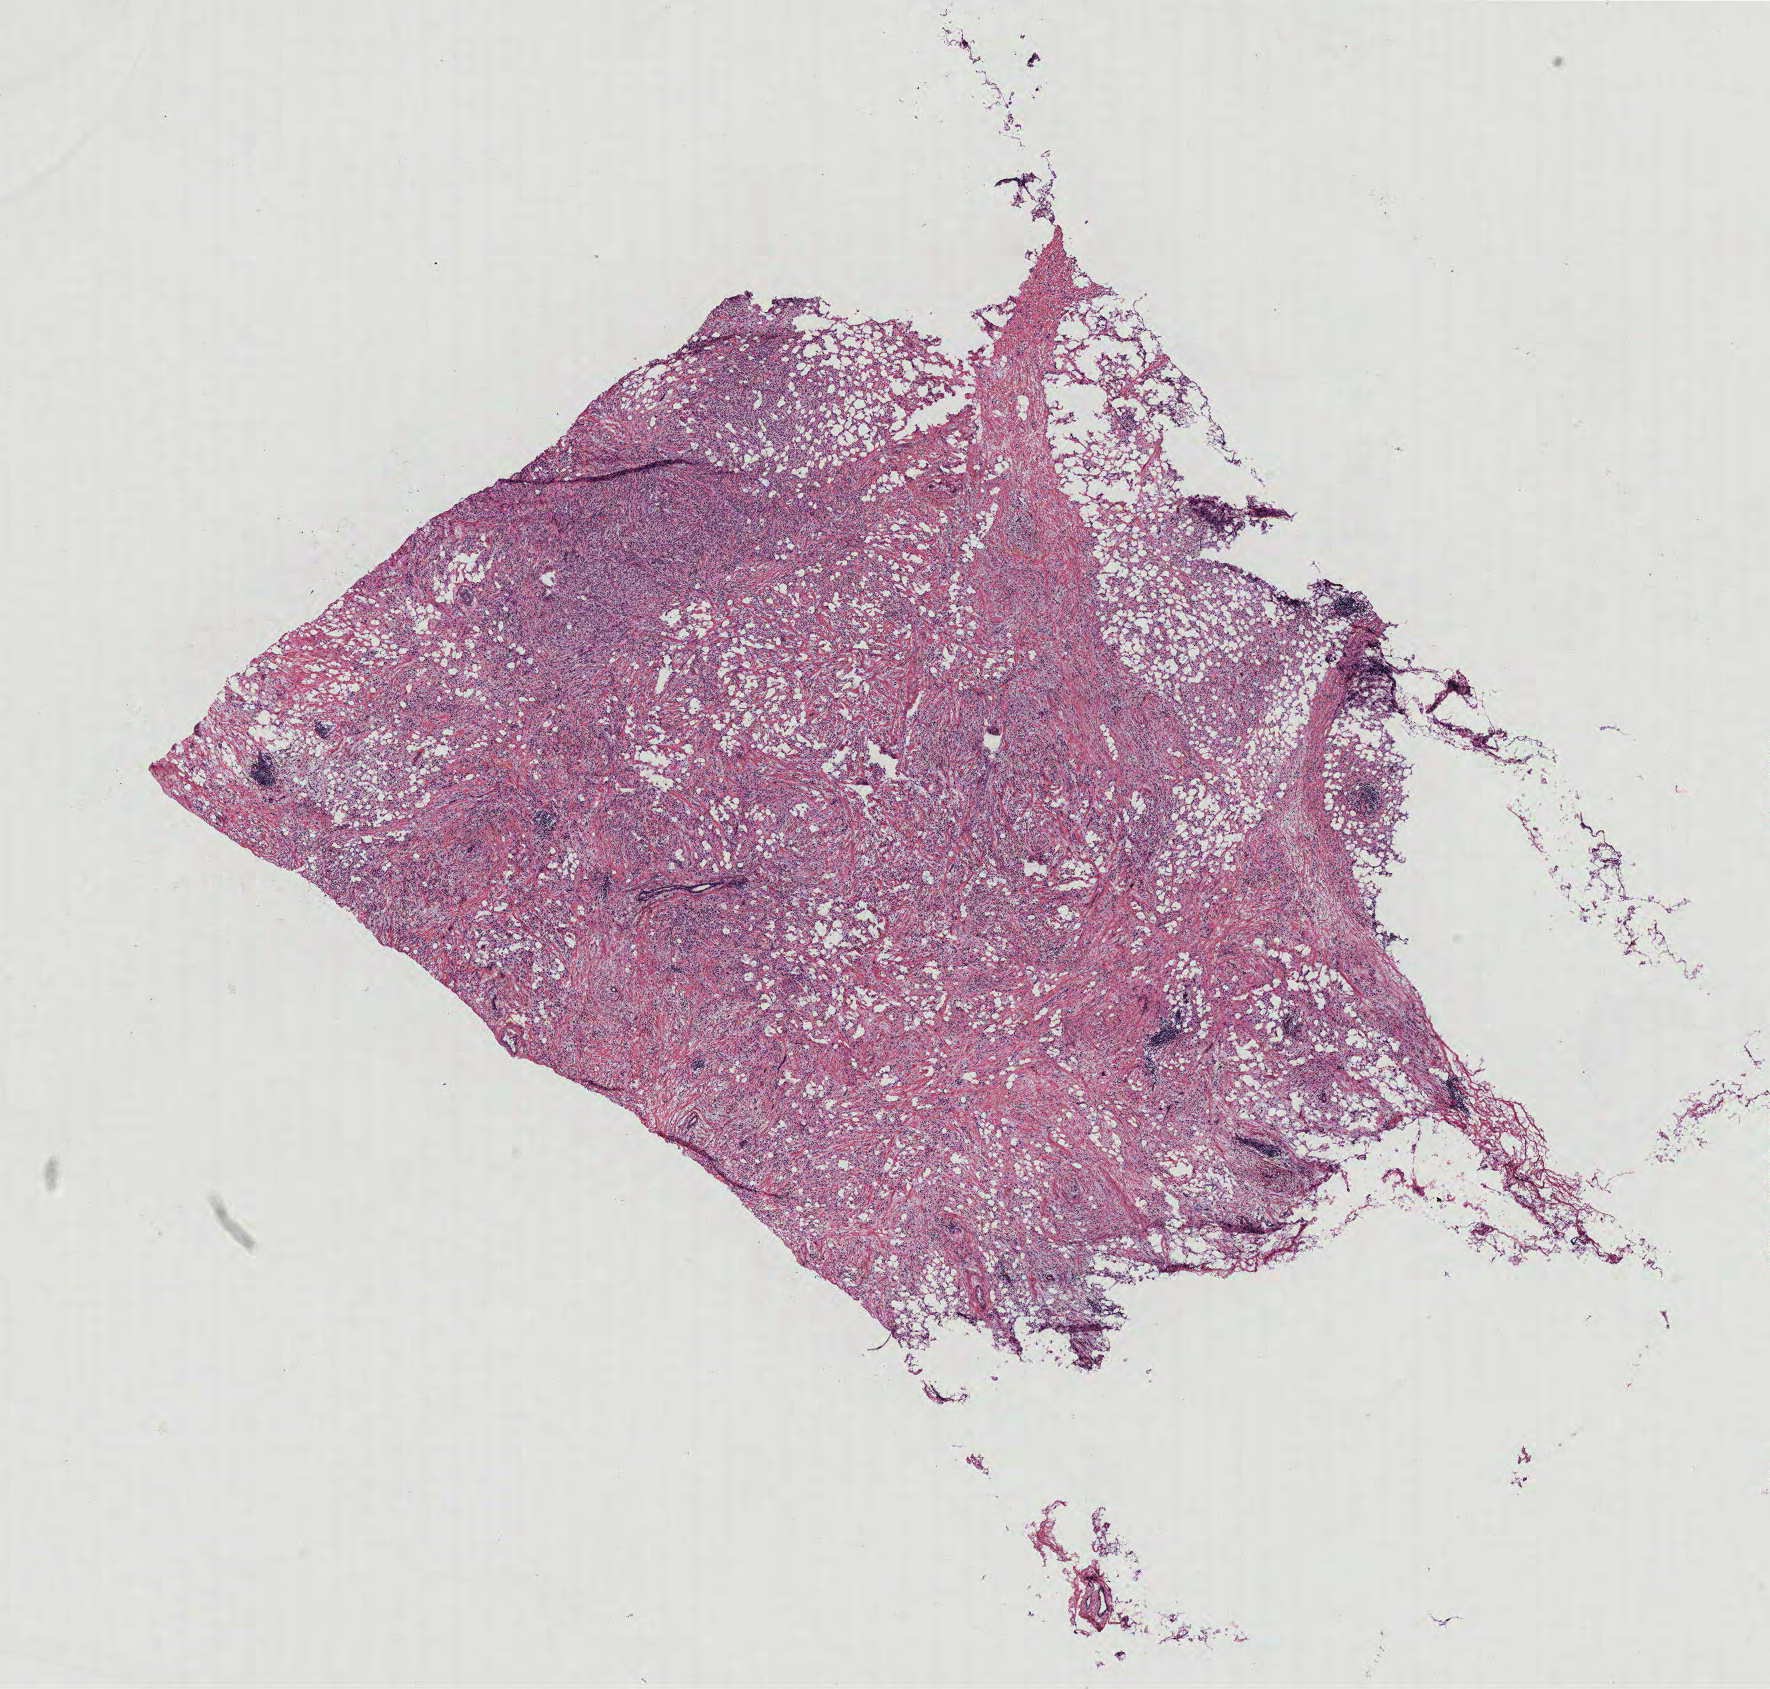
Whole-slide histology image, Hematoxylin and eosin (H&E) stained, shown as a low-resolution overview of the whole scanned area (about 14.2 x 13.5 mm, from a 40x scan), breast, tissue type not recorded. Female patient.
* patient diagnosis: Infiltrating duct carcinoma, NOS